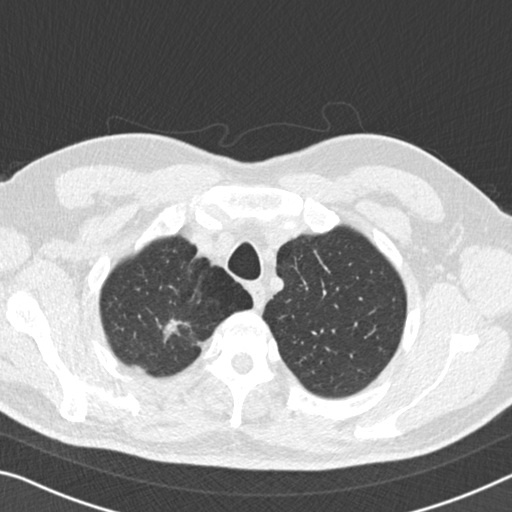
Low-dose screening chest CT, one axial slice; slice 143 of 167 in the series (ordered by position); reconstruction kernel B30f; 120 kVp; lung window (W 1500 / L -600 HU); 512 × 512 image matrix, field of view 336 × 336 mm.
Structures marked on this image (expert manual segmentation):
- lesion 1 (tumor, upper lobe of right lung): box from (x=164, y=320) to (x=181, y=337) px